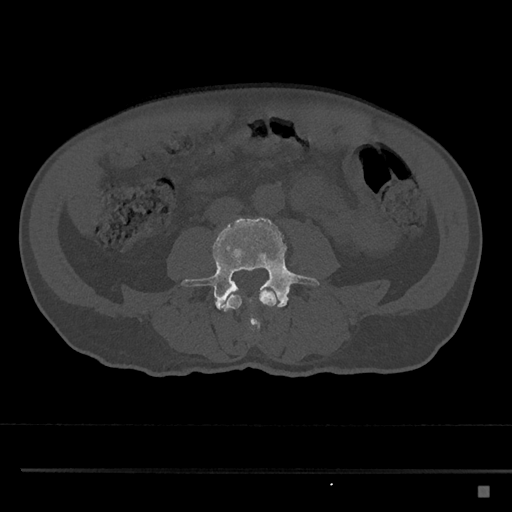
CT including the spine, one axial slice. Slice 654 of 797 in the series (ordered by position). Reconstruction kernel Br40s/3. 120 kVp. Bone window (W 1800 / L 400 HU). 0.5 mm slice thickness. 512 × 512 image matrix, field of view 391 × 391 mm. Patient: male, 59 years. Case-level facts recorded for this patient, not image findings: primary cancer: prostate.
Annotated regions visible in this slice (semi-automatically segmented with operator editing):
- L3 vertebra: bounding box [x1, y1, x2, y2] px = [219, 287, 278, 331]
- L4 vertebra: [181, 217, 319, 326]